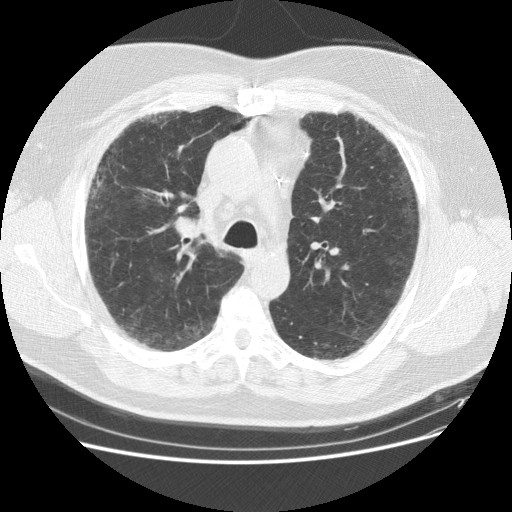
Chest CT (low-dose screening protocol), one axial image. First (baseline) screen. Lung window (W 1500 / L -600 HU). 2.5 mm slice thickness. Standard (soft-tissue) reconstruction kernel (STANDARD). Slice 43 of 151 in the series. 512 × 512 image matrix, field of view 378 × 378 mm. Male, age 59 years at enrolment.
• Expert-annotated lung lesion, bounding box <166,207,208,249> (left, top, right, bottom; pixels).
• The screening reader recorded 2 non-calcified nodules or masses ≥4 mm on this exam (right middle lobe, right lower lobe); which of them this box marks is not recorded.
• Lung cancer was diagnosed 338 days after this screen: adenocarcinoma, NOS, right upper lobe, right middle lobe, moderately differentiated (G2), stage IA (AJCC 6th edition), 13 mm at pathology.